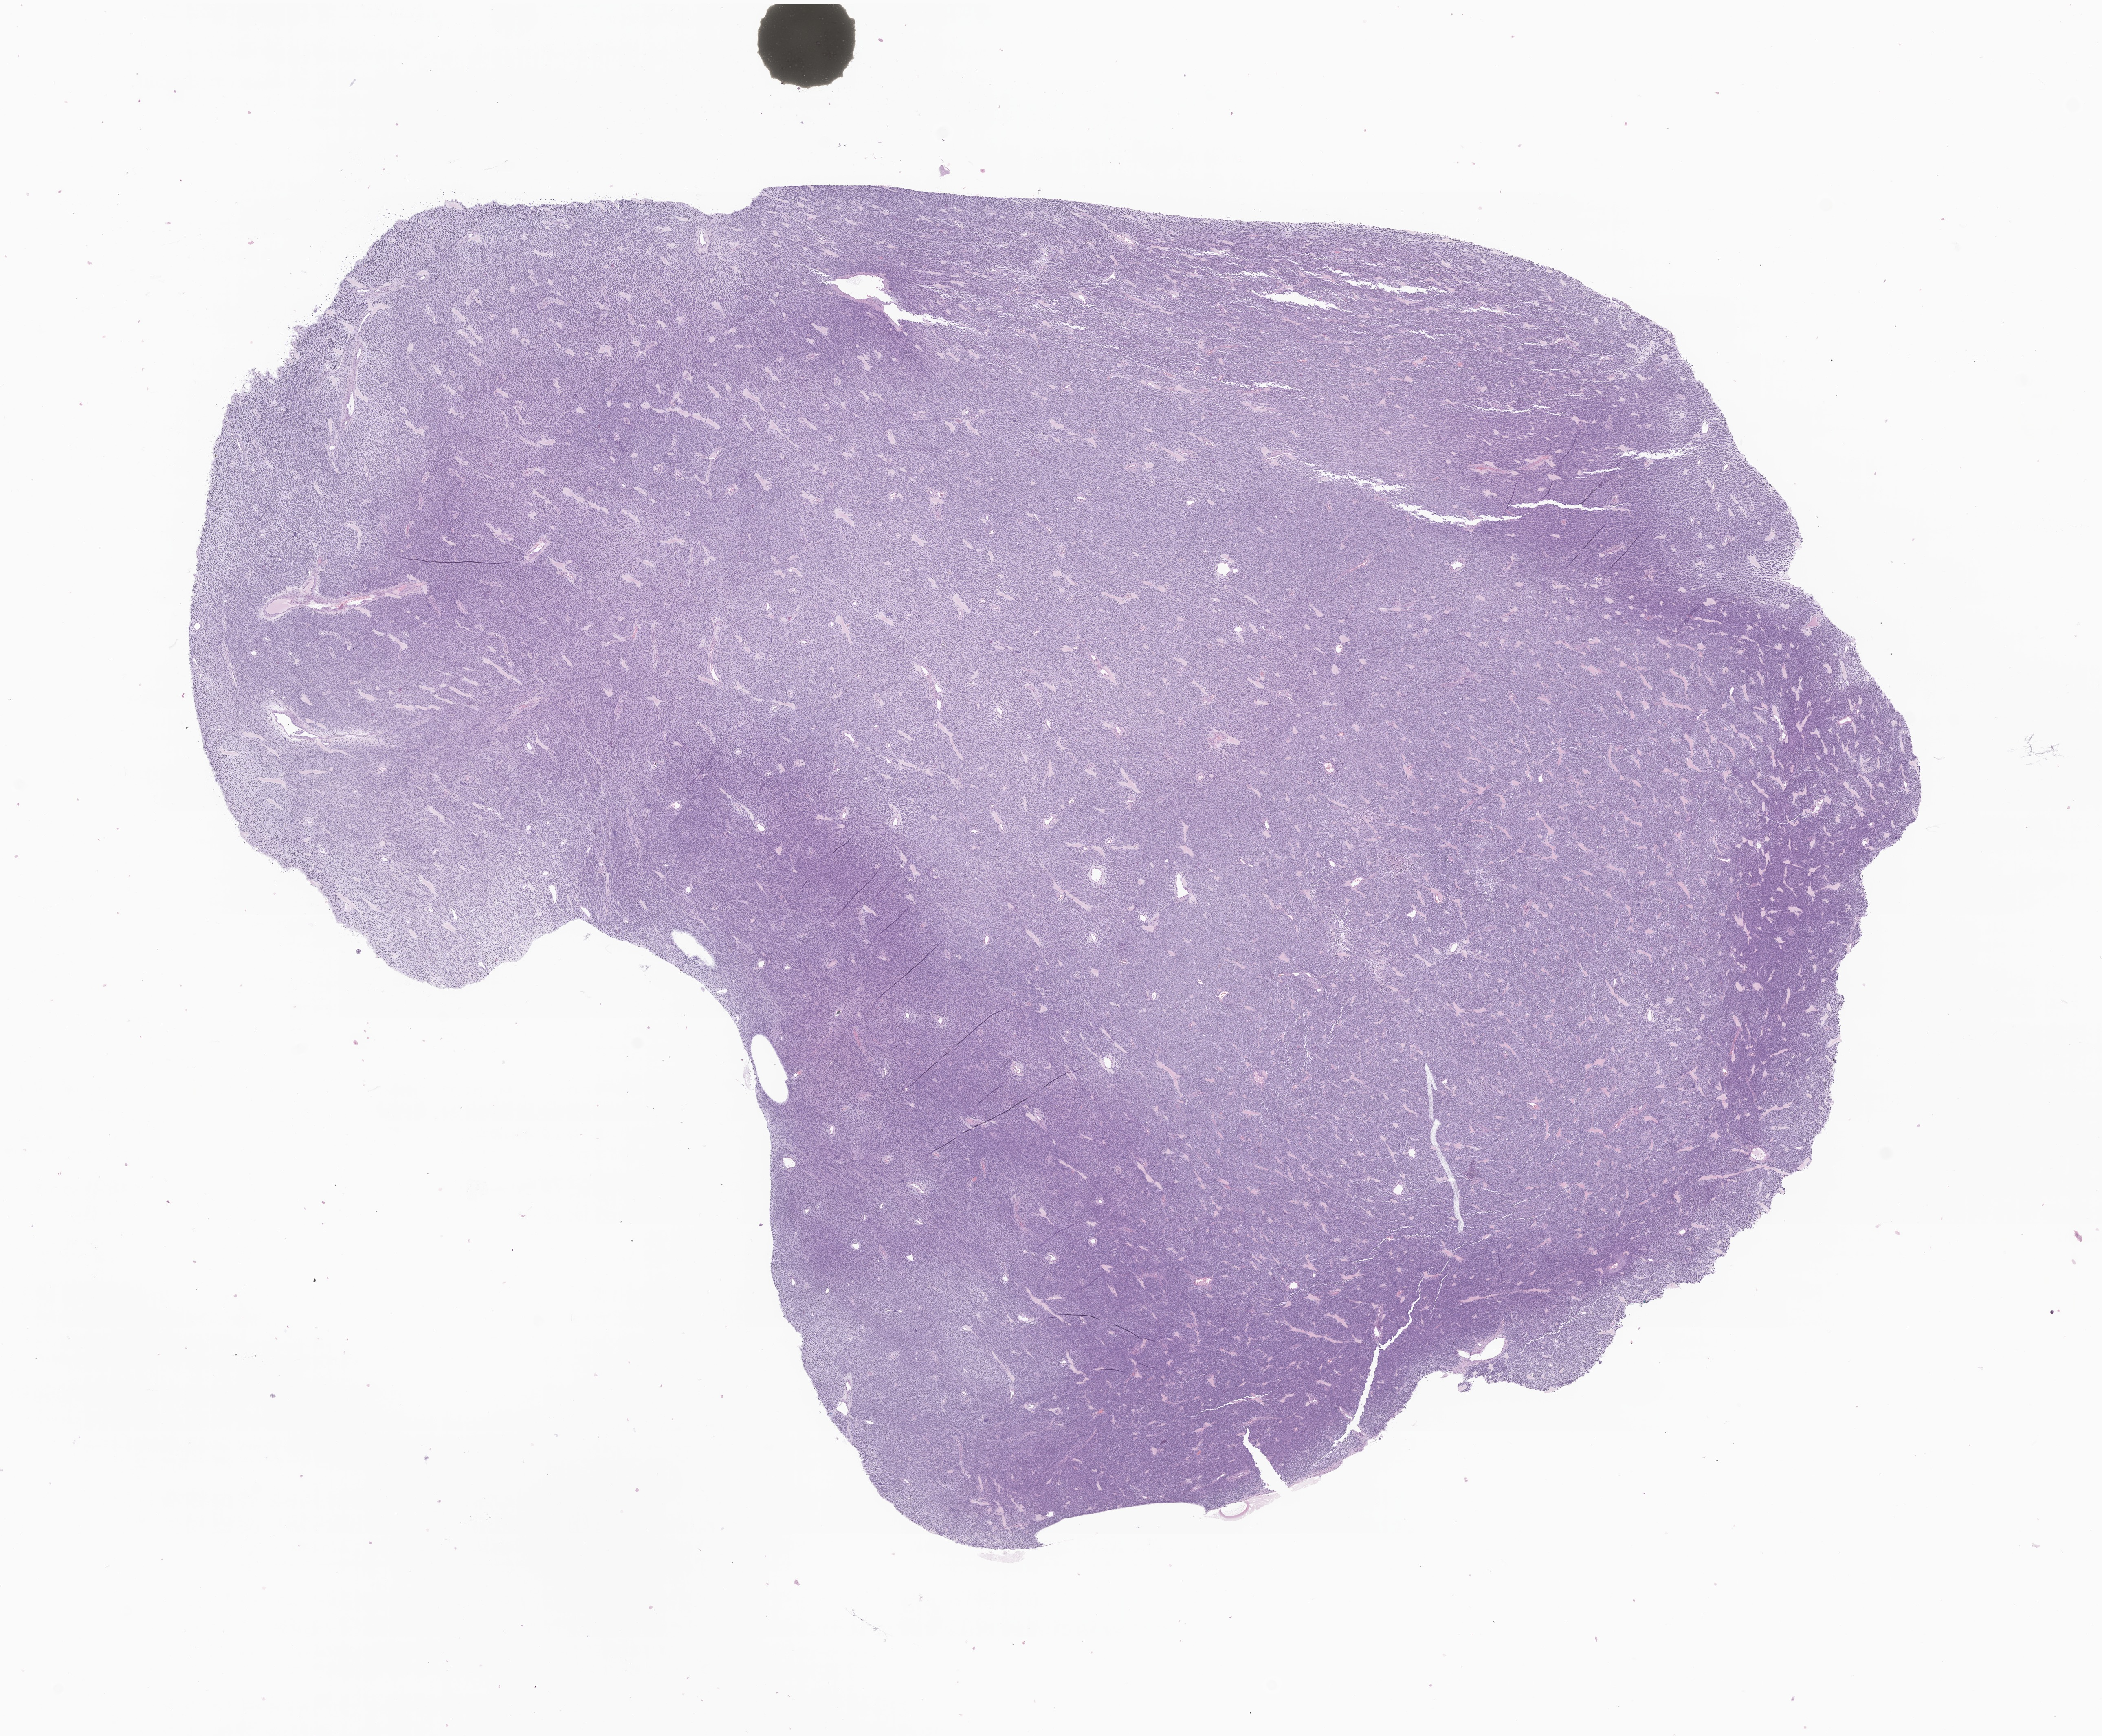
Haematoxylin and eosin whole-slide image of tumor tissue from the rib, sternum and/or clavicle, low-resolution overview of the scanned area, about 21.8 x 18.0 mm; FFPE section. Male patient, age 58 months.
- recorded diagnosis: Embryonal rhabdomyosarcoma, NOS